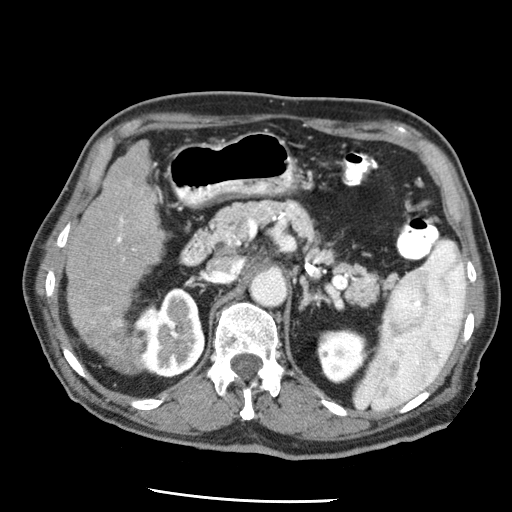
Contrast-enhanced abdominal CT (liver protocol), one axial slice. Position 22 of 79 along the scan axis. Soft-tissue window (W 400 / L 40 HU). 512 × 512 image matrix, field of view 320 × 320 mm. Case-level facts recorded for this patient, not image findings: diagnosis: hepatocellular carcinoma (patient treated with transarterial chemoembolisation; whether this scan precedes or follows treatment is not stated here); TNM stage (as recorded): Stage-IIIA; Child-Pugh class: A; tumour differentiation: moderately differentiated; tumour size: 7 cm.
Annotated regions visible in this slice (semi-automatically segmented with operator editing):
- liver parenchyma outside the tumour (the mass and vessels are separate outlines, so this box may not span the whole liver): box from (x=66, y=140) to (x=164, y=352) px
- liver vessels: (x=105, y=217)–(x=135, y=326)